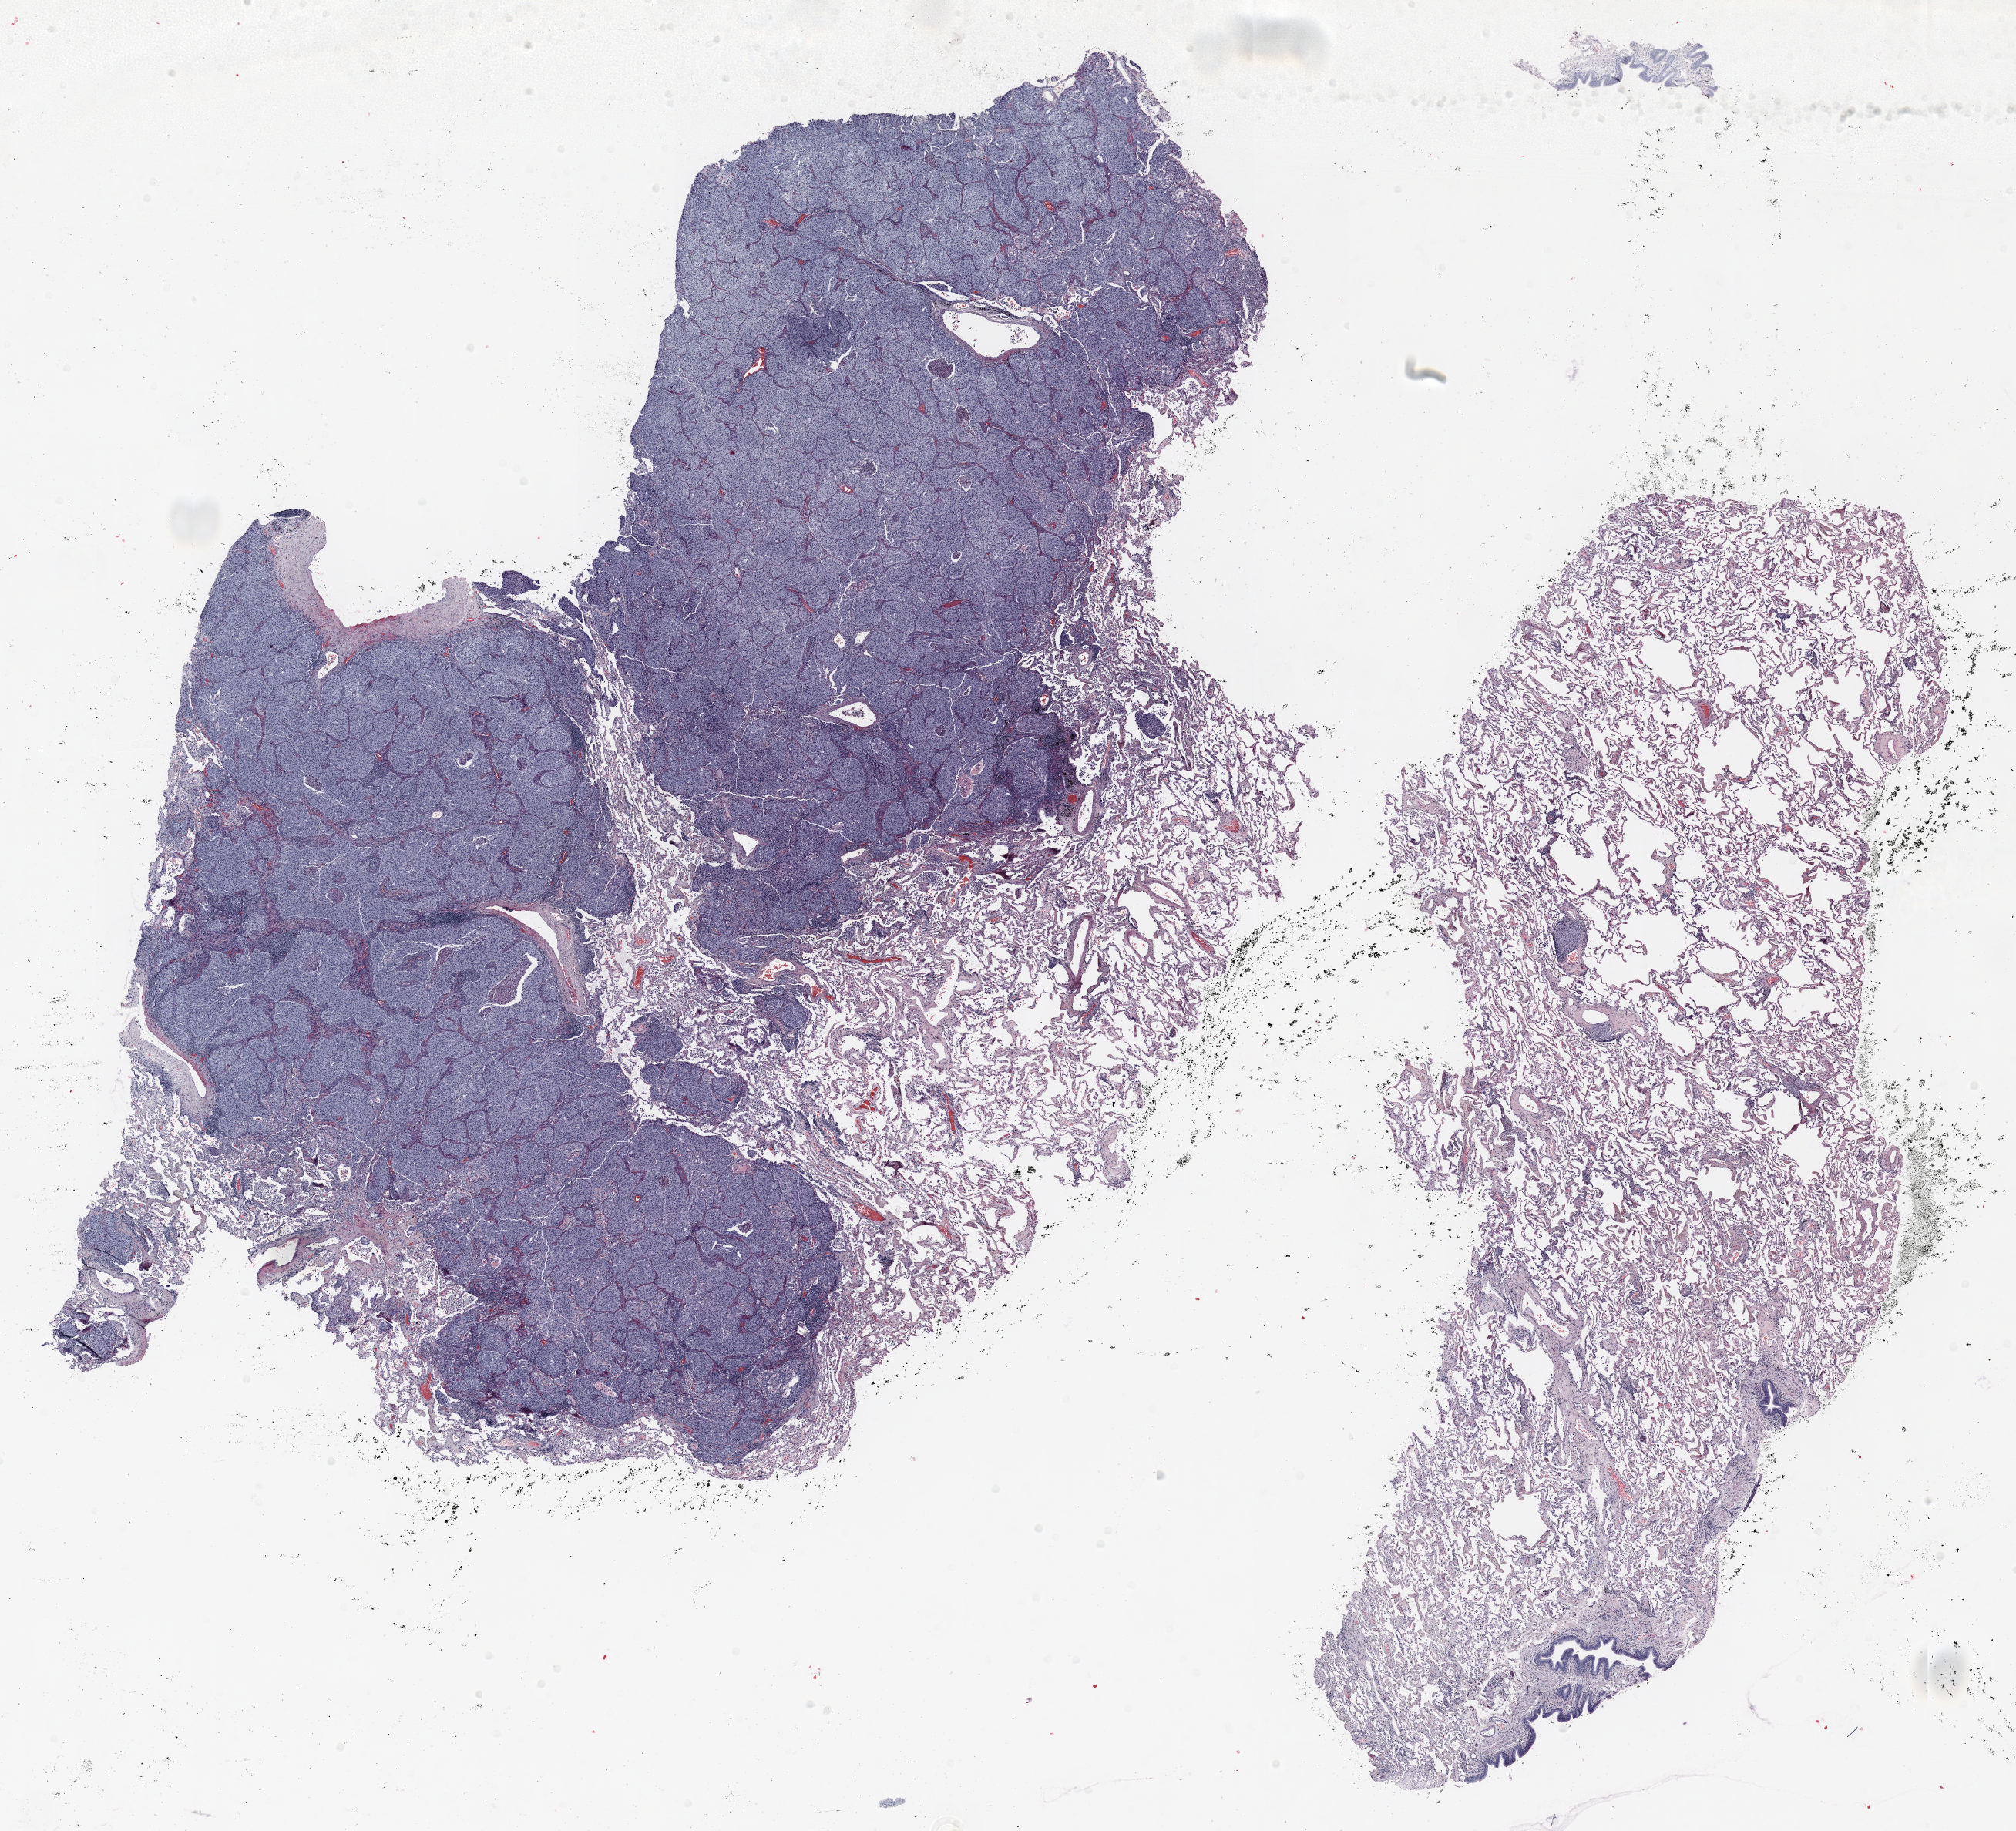
H&E-stained whole-slide image — shown as a low-resolution overview of the whole scanned area (about 21.0 x 19.1 mm, from a 20x scan); formalin-fixed paraffin-embedded (FFPE) section; lung. Male patient, aged 72 at enrolment. Former smoker at enrolment. Grade: moderately differentiated (G2).
Participant's lung-cancer diagnosis: Adenosquamous carcinoma. Tumour size (pathology): 53 mm. Stage (AJCC 6th edition): IIIA. Primary tumour location (clinical record): right upper lobe.